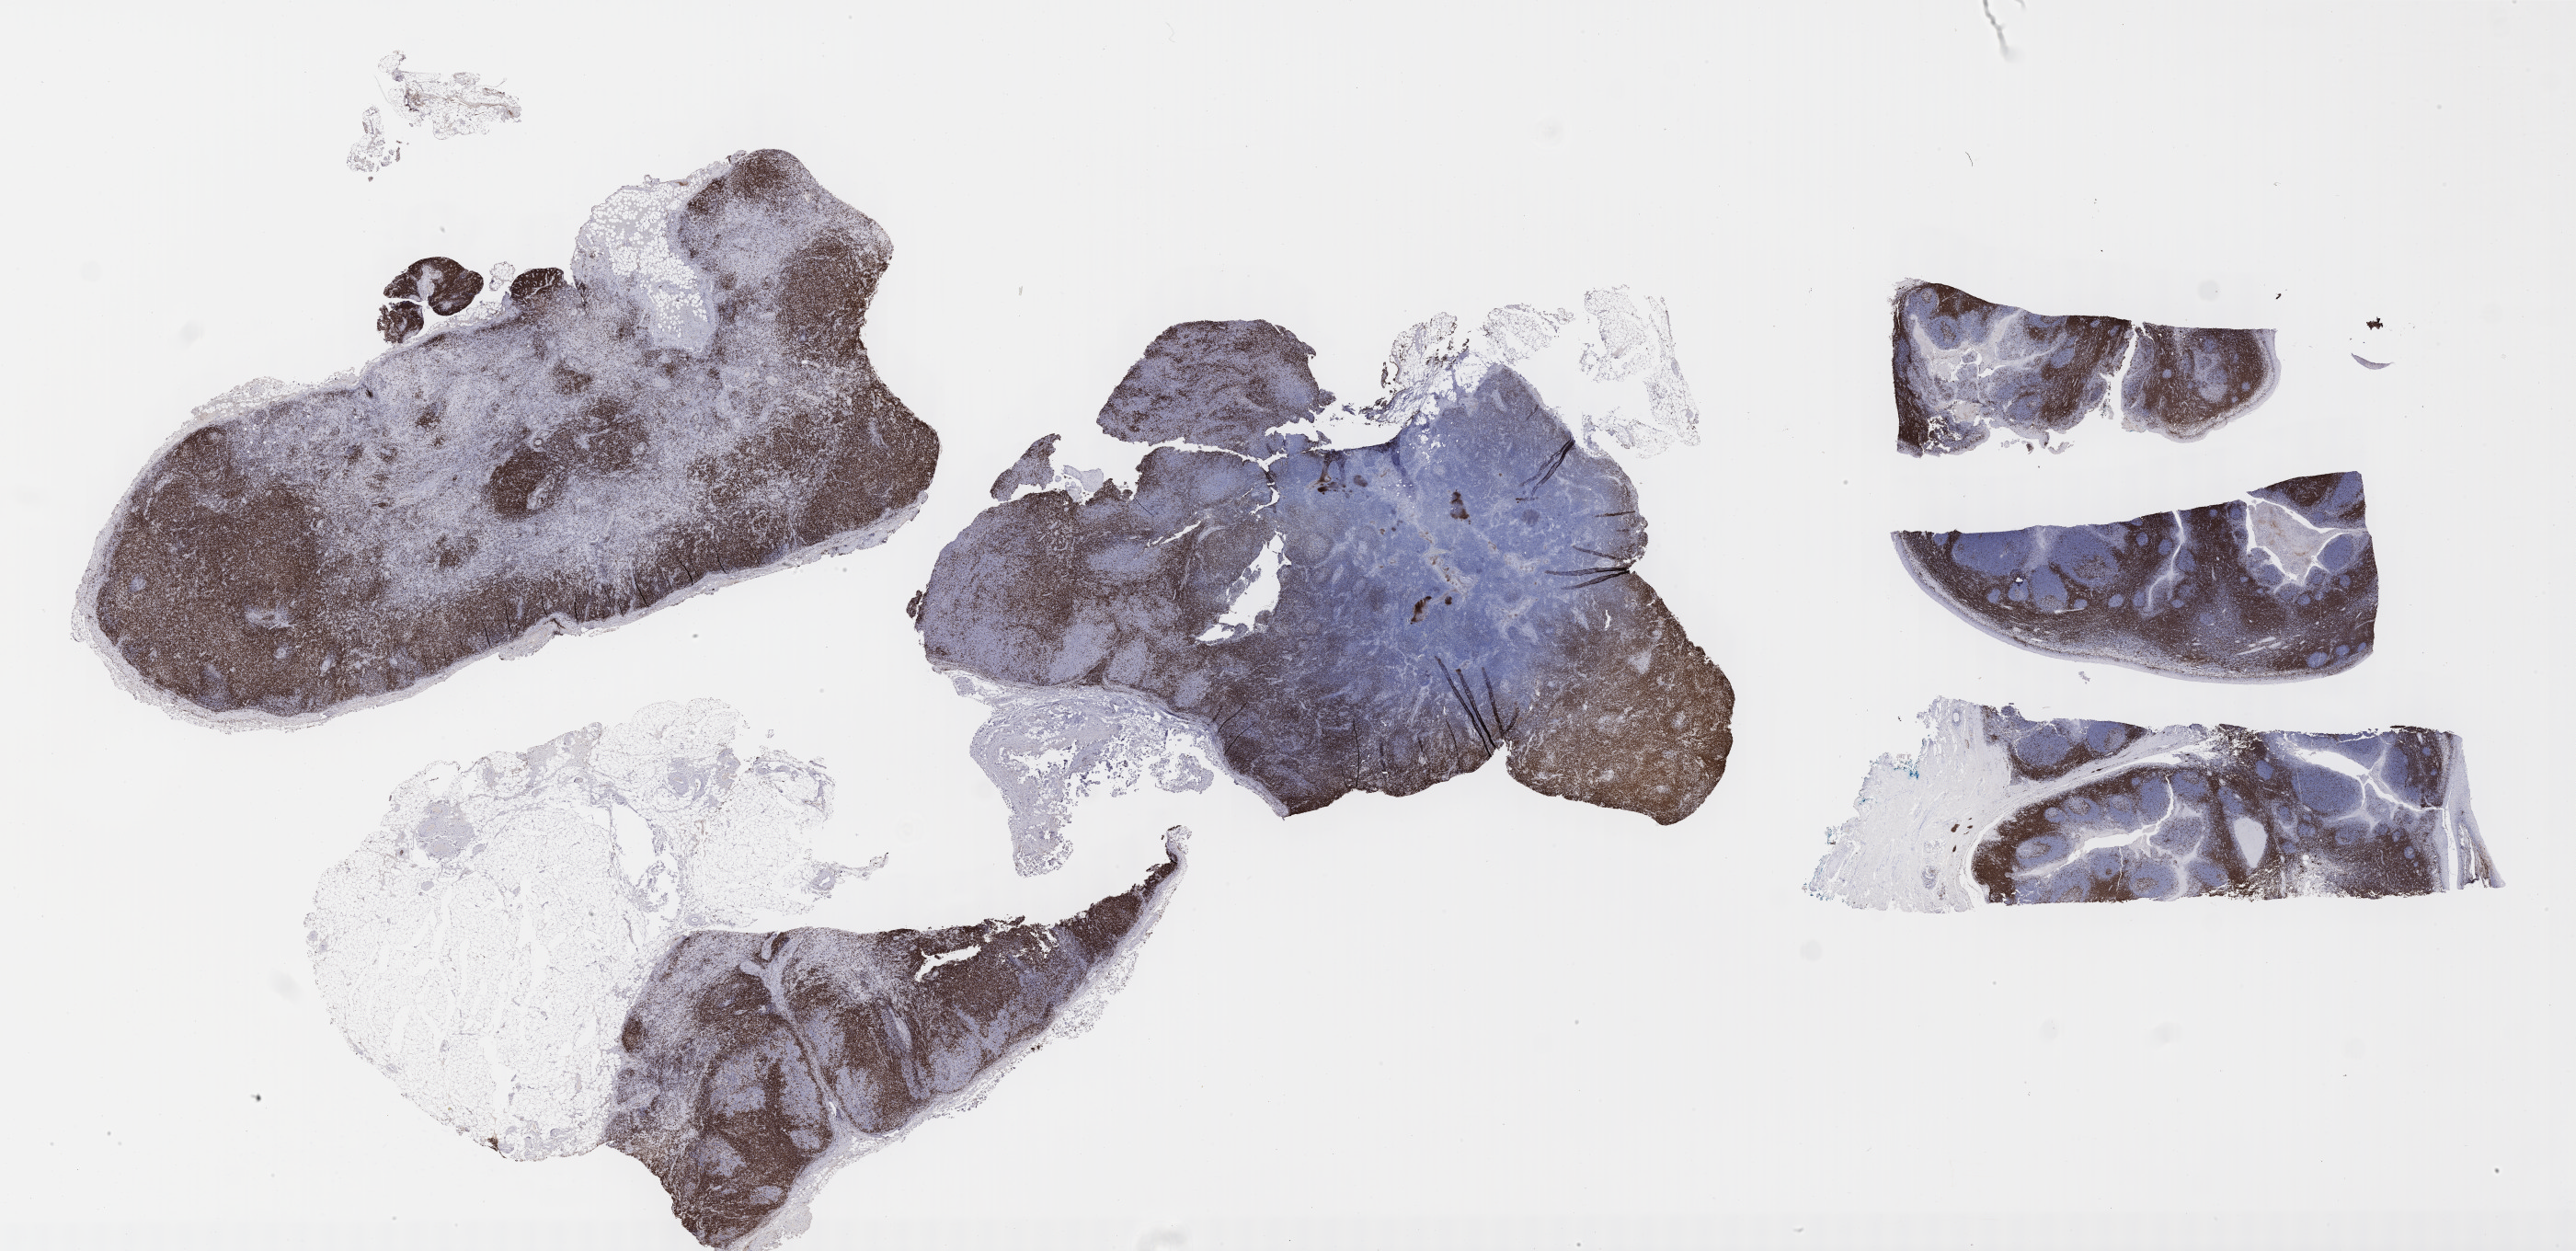
IHC for CD3, whole-slide image — shown as a low-resolution overview of the whole scanned area (about 45.3 x 22.0 mm); specimen: tumor tissue; anatomic site: lymph node. Male patient, 56 years old.
Diagnosis: Diffuse large B-cell lymphoma, NOS.